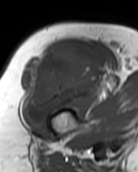
MRI of an extremity soft-tissue mass, one axial slice; slice 74 of 99 in the series (ordered by position); MR volume resampled by the dataset authors to the PET/CT grid (not the native acquisition matrix); 3.27 mm slice thickness; 138 × 172 image matrix, field of view 135 × 168 mm. Female patient. From the clinical record (not read from this slice): histological type: pleiomorphic undifferentiated sarcoma; grade: high; site of the primary tumour: right quadricep.
Annotated regions visible in this slice (expert contour drawn on MRI and transferred to this co-registered scan by the dataset authors):
- gross tumour volume including surrounding oedema: bounding box [x1, y1, x2, y2] px = [23, 45, 100, 120]
- gross tumour volume (mass): [23, 45, 100, 120]